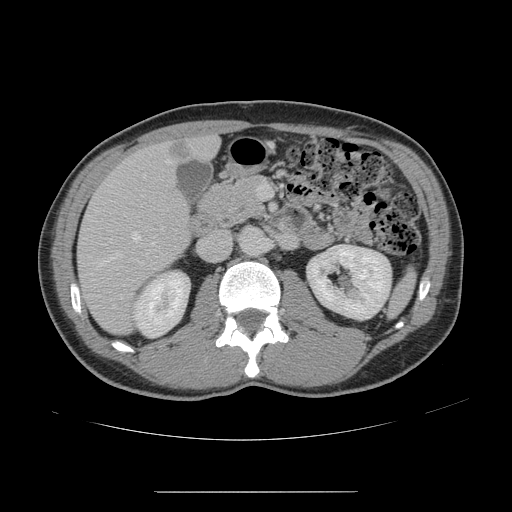
Contrast-enhanced abdominal CT, one axial slice; slice 69 of 178 in the series (ordered by position); soft-tissue window (W 400 / L 40 HU); 2.5 mm slice thickness; 512 × 512 image matrix, field of view 401 × 401 mm. Male patient, age 53 years. From the clinical record (not read from this slice): diagnosis: colorectal cancer liver metastases, imaged before liver resection; multiple liver metastases: yes; largest metastasis: 2.4 cm; chemotherapy before resection: yes.
Annotated regions visible in this slice (expert manual segmentation):
- hepatic veins: box from (x=94, y=159) to (x=170, y=268) px
- liver: (x=79, y=137)–(x=218, y=333)
- planned liver remnant (the part of the liver to remain after resection): (x=195, y=137)–(x=218, y=159)
- portal vein (with intrahepatic branches): (x=257, y=184)–(x=267, y=199)
- liver metastasis: (x=170, y=142)–(x=193, y=160)